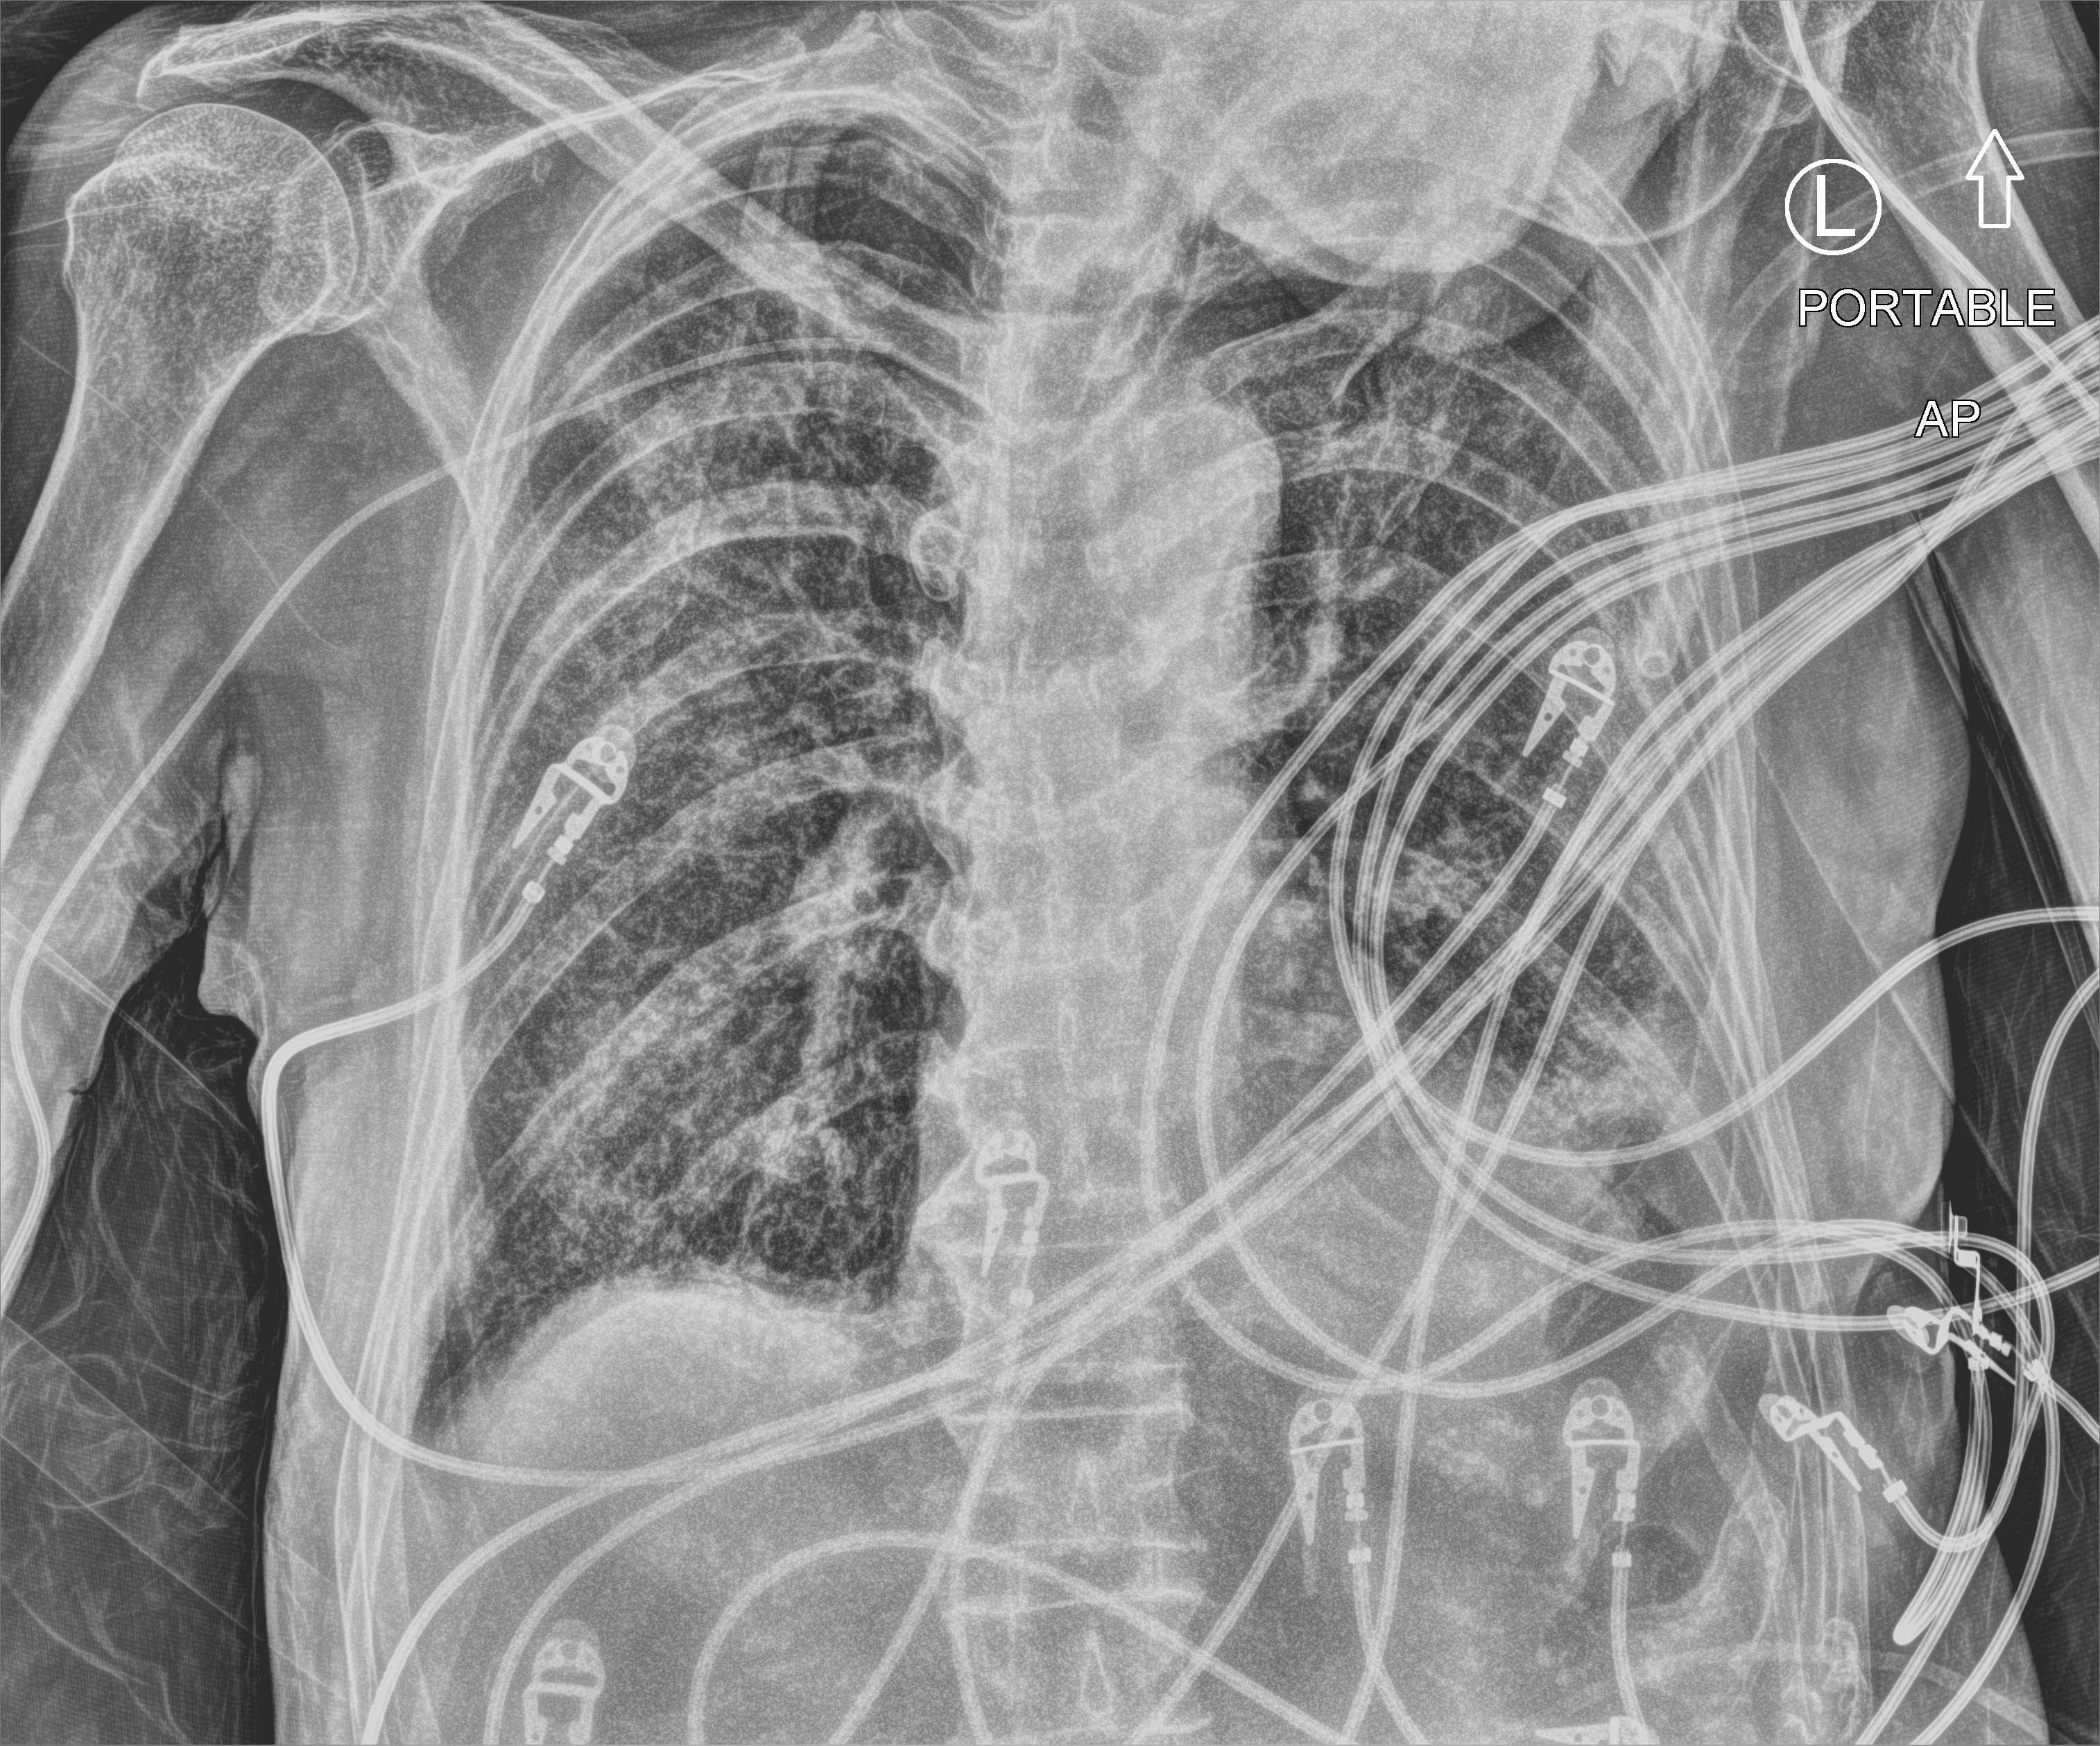
Bedside chest radiograph (computed radiography). Patient hospitalised with COVID-19; male, aged 60–74 years.
Admission-level facts for this patient (not findings on this image; timing relative to this image not recorded): mechanically ventilated during this hospital stay: yes.